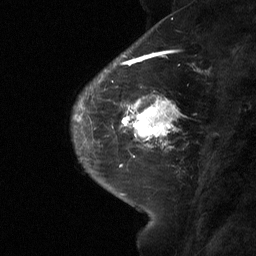
Breast MRI (dynamic contrast-enhanced), one sagittal slice. Dynamic contrast-enhanced study with each time point stored as its own series, time point 2 of 3 at this slice position (early post-contrast, ordered by acquisition time). 1.5 T. TE 4.8 ms, TR 27 ms. 2 mm slice thickness. 256 × 256 image matrix, field of view 180 × 180 mm. Female patient, age 42 years. From the clinical record (not read from this slice): setting: breast cancer imaged before/during neoadjuvant chemotherapy; receptor status: triple-negative.
Outlined on this slice (semi-automatic segmentation, software-assisted and operator-edited):
- analysis volume of interest (the breast-tissue region the enhancement analysis was run in; not a lesion): bounding box (x1, y1, x2, y2) in pixels: (115, 85, 177, 160)
- tumour enhancement mask (voxels above the 90 % enhancement threshold inside the analysis volume of interest): (121, 96, 173, 157)